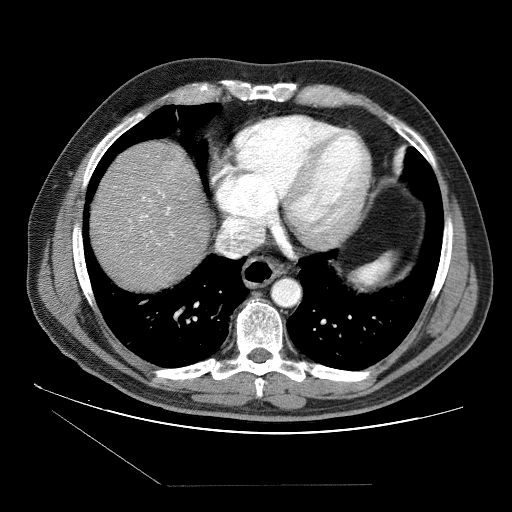
Contrast-enhanced abdominal CT (liver protocol), one axial slice; position 76 of 87 along the scan axis; reconstruction kernel STANDARD; 120 kVp; soft-tissue window (W 400 / L 40 HU); 2.5 mm slice thickness; 512 × 512 image matrix. From the clinical record (not read from this slice): diagnosis: hepatocellular carcinoma (patient treated with transarterial chemoembolisation; whether this scan precedes or follows treatment is not stated here); TNM stage (as recorded): Stage-II; Child-Pugh class: B; tumour differentiation: no biopsy; tumour nodularity: multinodular.
Annotated regions visible in this slice (semi-automatically segmented with operator editing):
- liver parenchyma outside the tumour (the mass and vessels are separate outlines, so this box may not span the whole liver): bounding box [x1, y1, x2, y2] px = [90, 140, 210, 290]
- liver vessels: [129, 190, 173, 245]